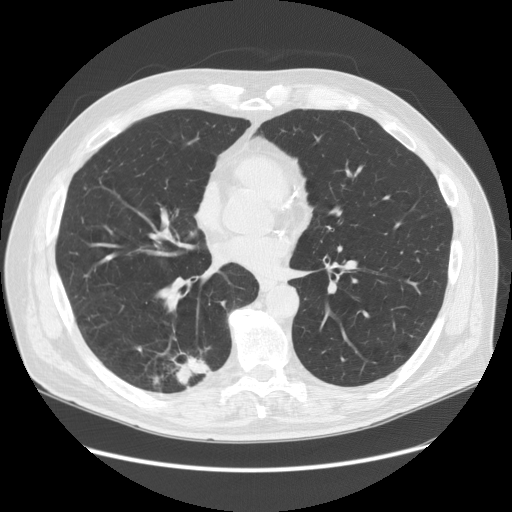
Low-dose screening chest CT, axial slice; first (baseline) screen; lung window (W 1500 / L -600 HU); 2.5 mm slice thickness; slice 82 of 149 in the series. Male, age 68 years at enrolment.
Expert-annotated lung lesion, bounding box [x1, y1, x2, y2] px = [123, 333, 225, 407]. Screening reader's record for this exam (one nodule recorded; not confirmed to be the boxed lesion): non-calcified nodule or mass ≥4 mm, right lower lobe, 37 × 20 mm, spiculated (stellate) margins, soft tissue attenuation.